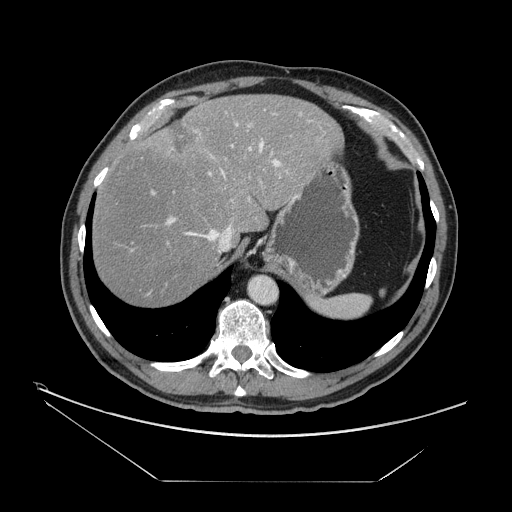
Contrast-enhanced abdominal CT, one axial slice; position 121 of 161 along the scan axis; reconstruction kernel STANDARD; 120 kVp; intravenous contrast given; soft-tissue window (W 400 / L 40 HU); 2.5 mm slice thickness; 512 × 512 image matrix, field of view 440 × 440 mm. Male patient, age 65 years. From the clinical record (not read from this slice): diagnosis: colorectal cancer liver metastases, imaged before liver resection.
Outlined on this slice (manually delineated by an expert):
- hepatic veins: bounding box <184,142,263,253> (left, top, right, bottom; pixels)
- liver: <92,94,340,309>
- planned liver remnant (the part of the liver to remain after resection): <92,94,340,309>
- portal vein (with intrahepatic branches): <152,109,302,226>
- liver metastasis: <173,123,196,155>